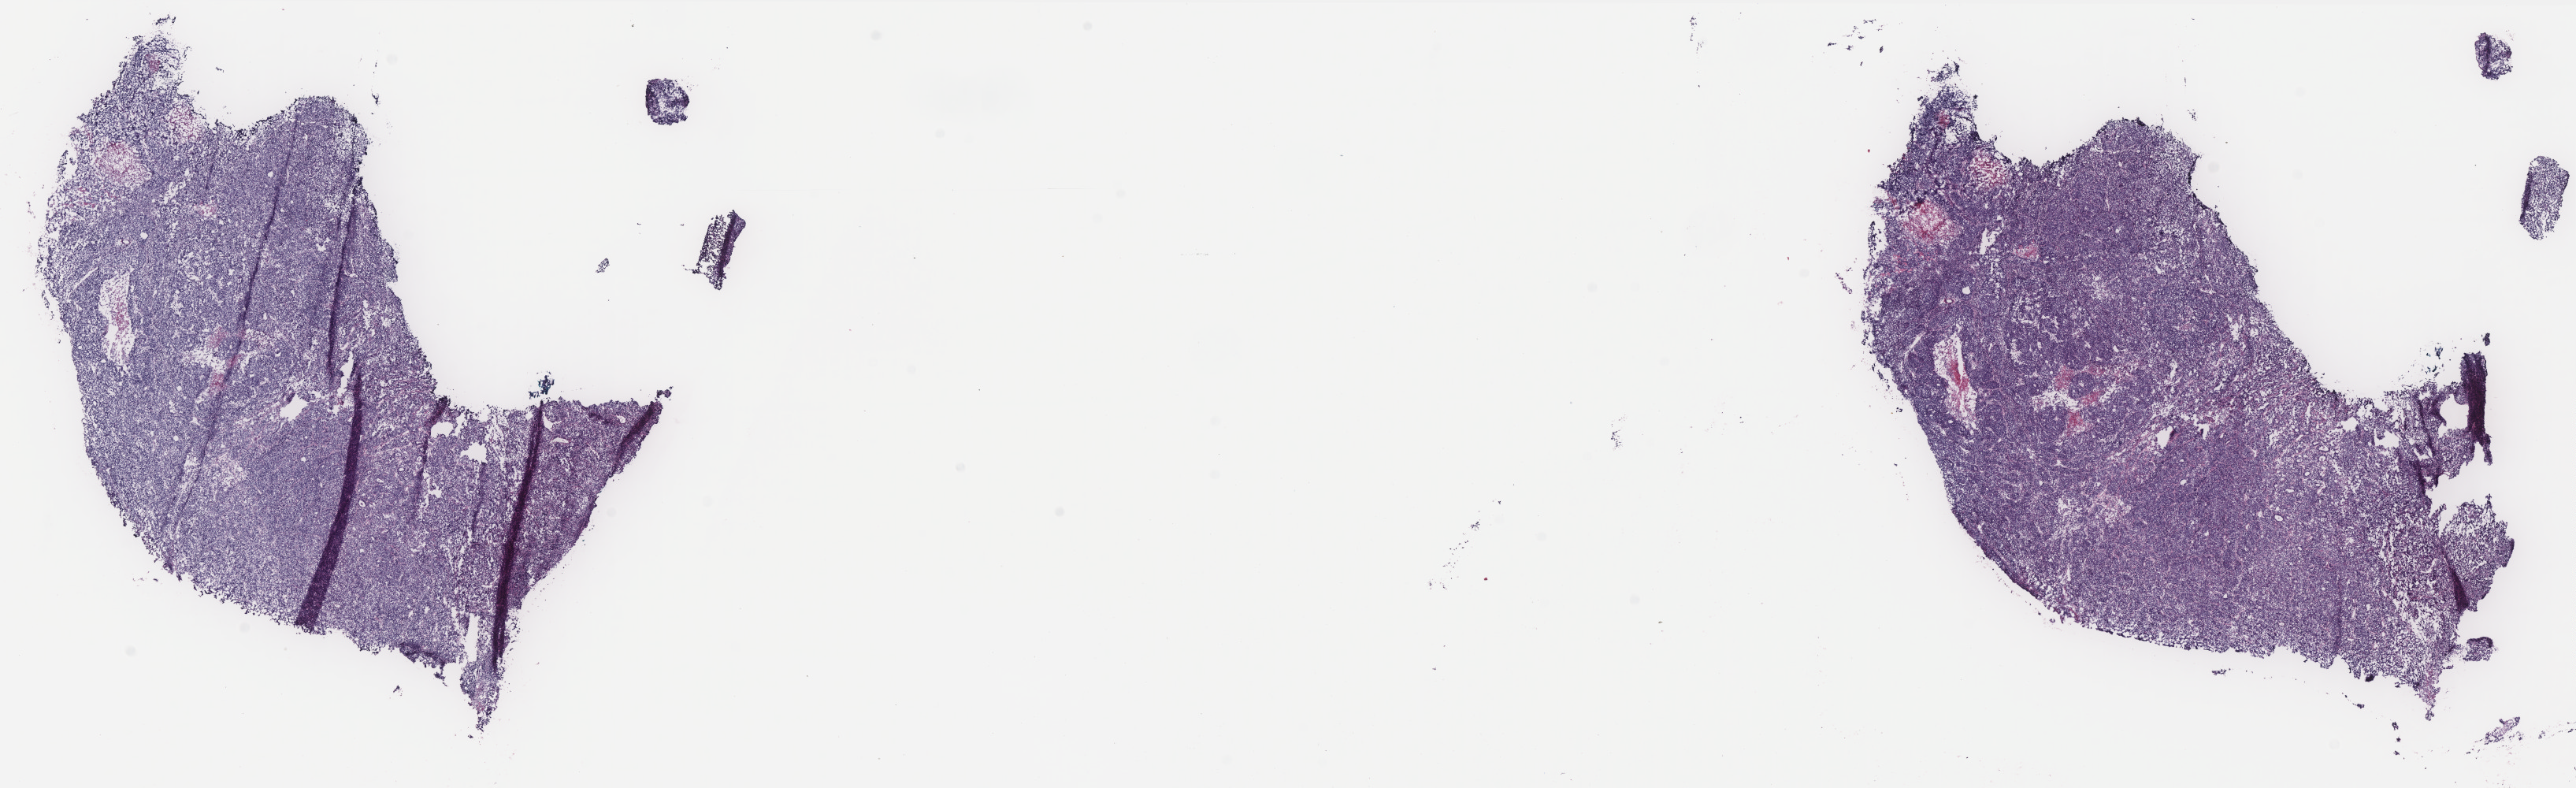
Whole-slide histology image, H&E, whole scanned area (about 26.2 x 8.0 mm, from a 40x scan) shown as a low-resolution overview; frozen section from the bottom of the tissue portion; sample: primary tumour, uterus. Female, age 65 years at initial diagnosis. Histologic grade: G3 (poorly differentiated). Slide review estimates, as recorded: tumour cells 82%, tumour nuclei 92%, normal cells 0%, stromal cells 8%, necrosis 10%. Infiltration values recorded for this section: lymphocyte infiltration 3%, monocyte infiltration 0%, neutrophil infiltration 0%.
* FIGO stage: IB
* histologic diagnosis: Endometrioid adenocarcinoma, NOS (endometrium)